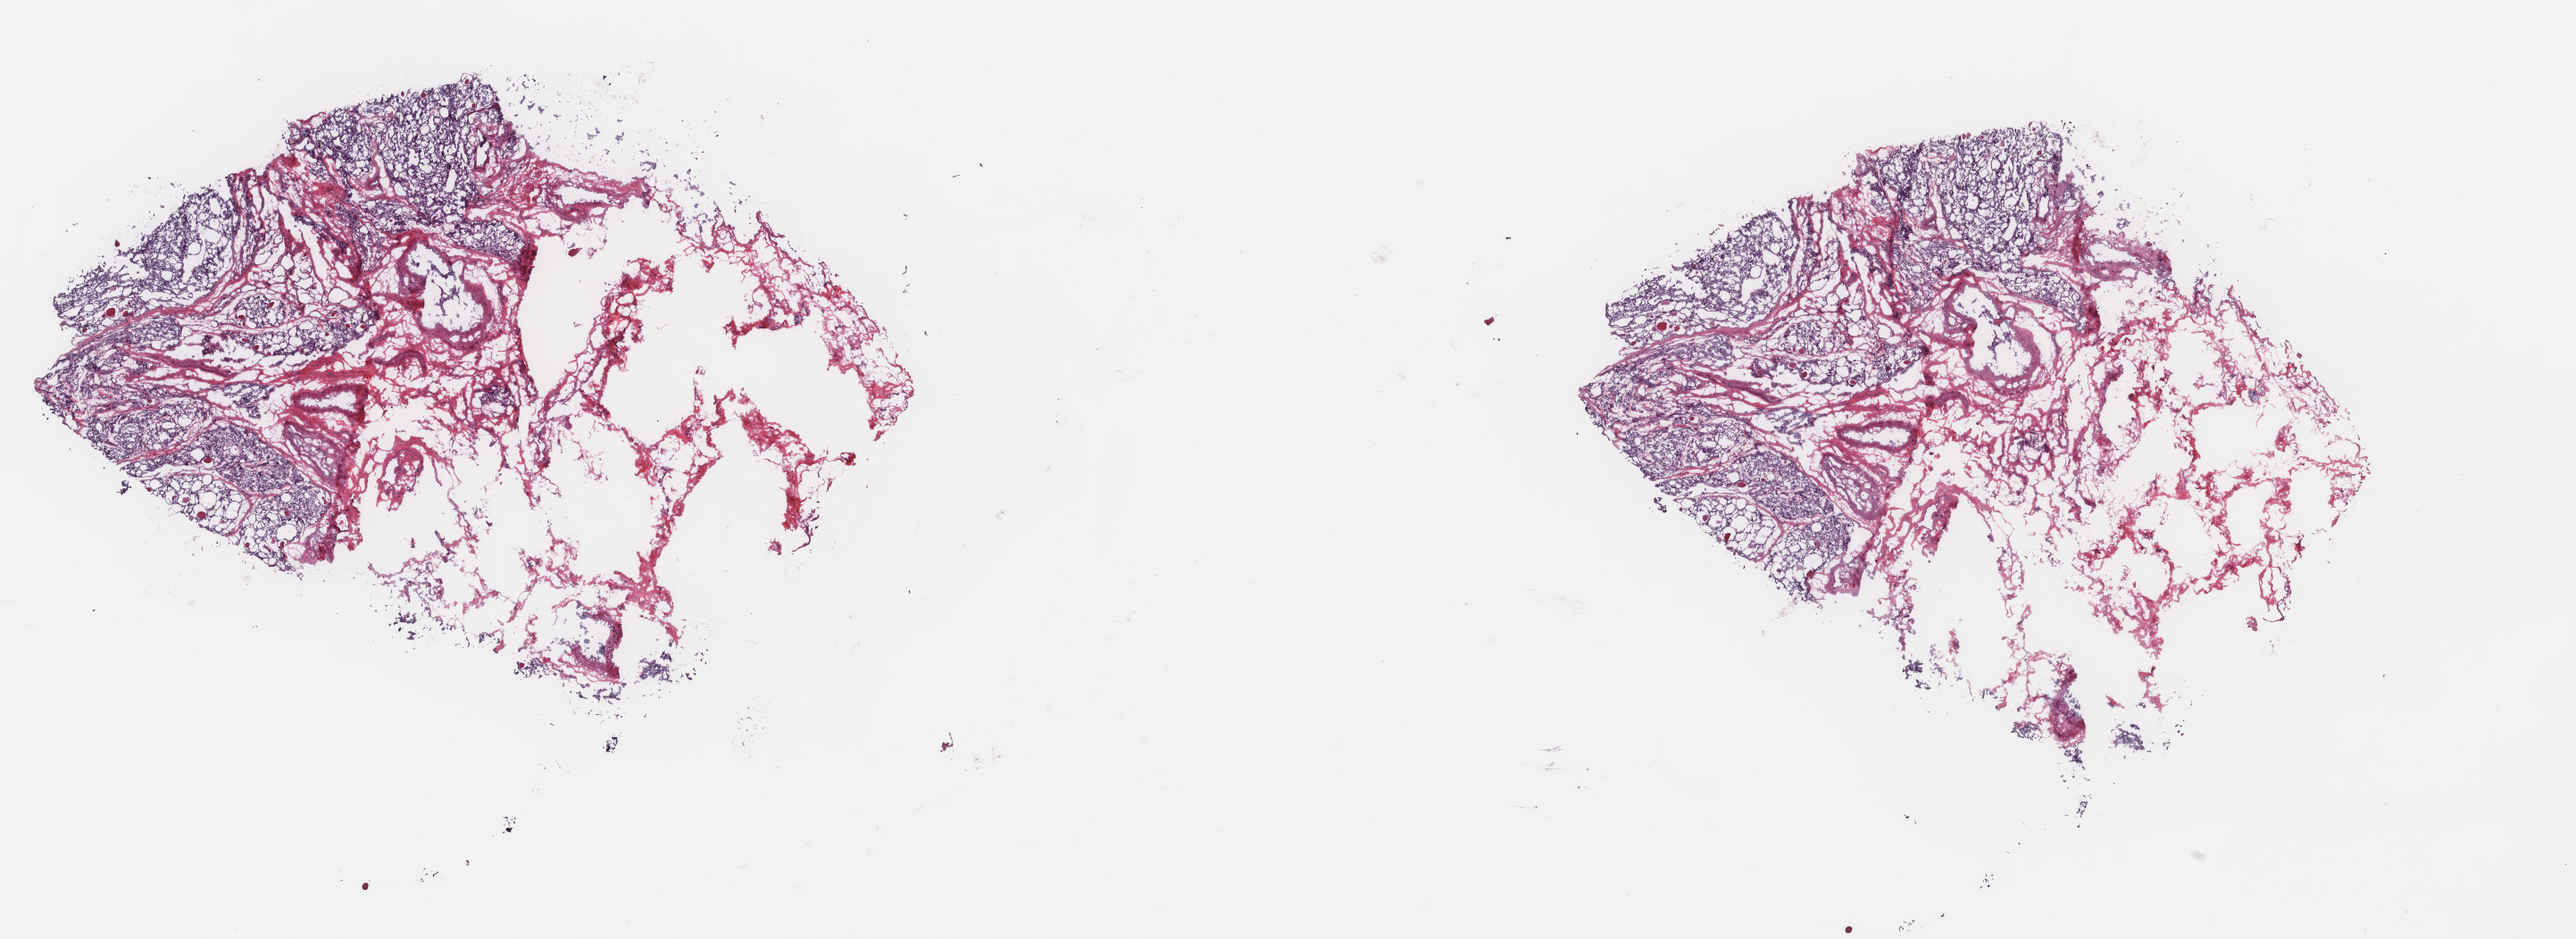
Digitized H&E tissue section (whole slide), a low-resolution overview of the entire scanned area, about 22.9 x 8.4 mm (acquisition: 40x scan). Frozen section from the top of the tissue portion. Thyroid, primary tumour sample. Male patient; age at initial diagnosis 62 years. Composition of this section per pathologist review: tumour cells 40%, tumour nuclei 70%, normal cells 50%, stromal cells 10%, necrosis 0%. Infiltration values recorded for this section: lymphocyte infiltration 1%, monocyte infiltration 1%, neutrophil infiltration 0%.
- AJCC pathologic stage: IVA
- pathologic diagnosis: Papillary adenocarcinoma, NOS (thyroid gland)
- lymph nodes positive (case pathology): 31 of 75 examined
- TNM: T3 N1b M0